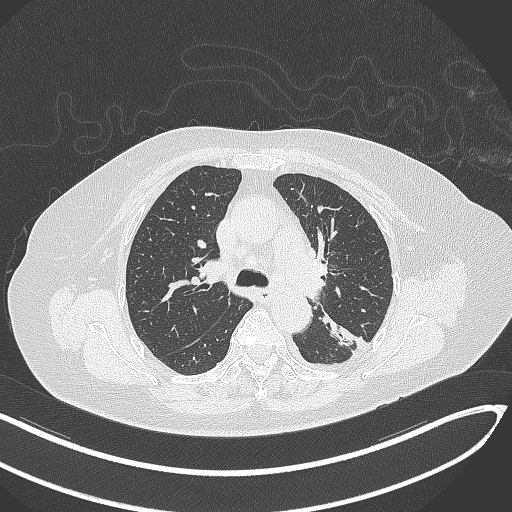
Chest CT, one axial slice. Reconstruction kernel B70f. 120 kVp. Lung window (W 1500 / L -600 HU). 1 mm slice thickness. 512 × 512 image matrix, field of view 400 × 400 mm. Female patient, age 76 years. From the clinical record (not read from this slice): clinical TNM (as recorded): T1c N0 M0.
Outlined on this slice (bounding box drawn by a radiologist):
- lung tumour (recorded histology: adenocarcinoma): bounding box <319,311,355,354> (left, top, right, bottom; pixels)